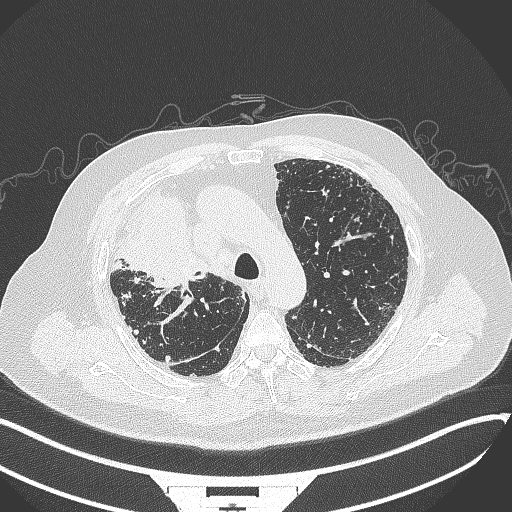
Chest CT, one axial slice. Reconstruction kernel B70f. Lung window (W 1500 / L -600 HU). 1 mm slice thickness. 512 × 512 image matrix, field of view 400 × 400 mm. Patient: male, 69 years. From the clinical record (not read from this slice): clinical TNM (as recorded): T4 N3 M1.
Structures marked on this image (rectangle marked by the reading radiologist):
- lung tumour (recorded histology: adenocarcinoma): bounding box <110,189,203,288> (left, top, right, bottom; pixels)